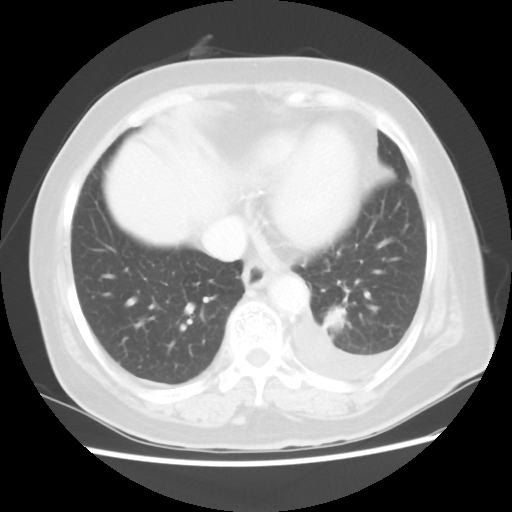
Chest CT, one axial slice. Slice 16 of 80 in the series (ordered by position). Reconstruction kernel STANDARD. 100 kVp. Lung window (W 1500 / L -600 HU). 512 × 512 image matrix. Patient: female, 68 years. Case-level facts recorded for this patient, not image findings: clinical TNM (as recorded): T1c N0 M1.
Outlined on this slice (rectangle marked by the reading radiologist):
- lung tumour (recorded histology: adenocarcinoma): box from (x=321, y=303) to (x=351, y=339) px